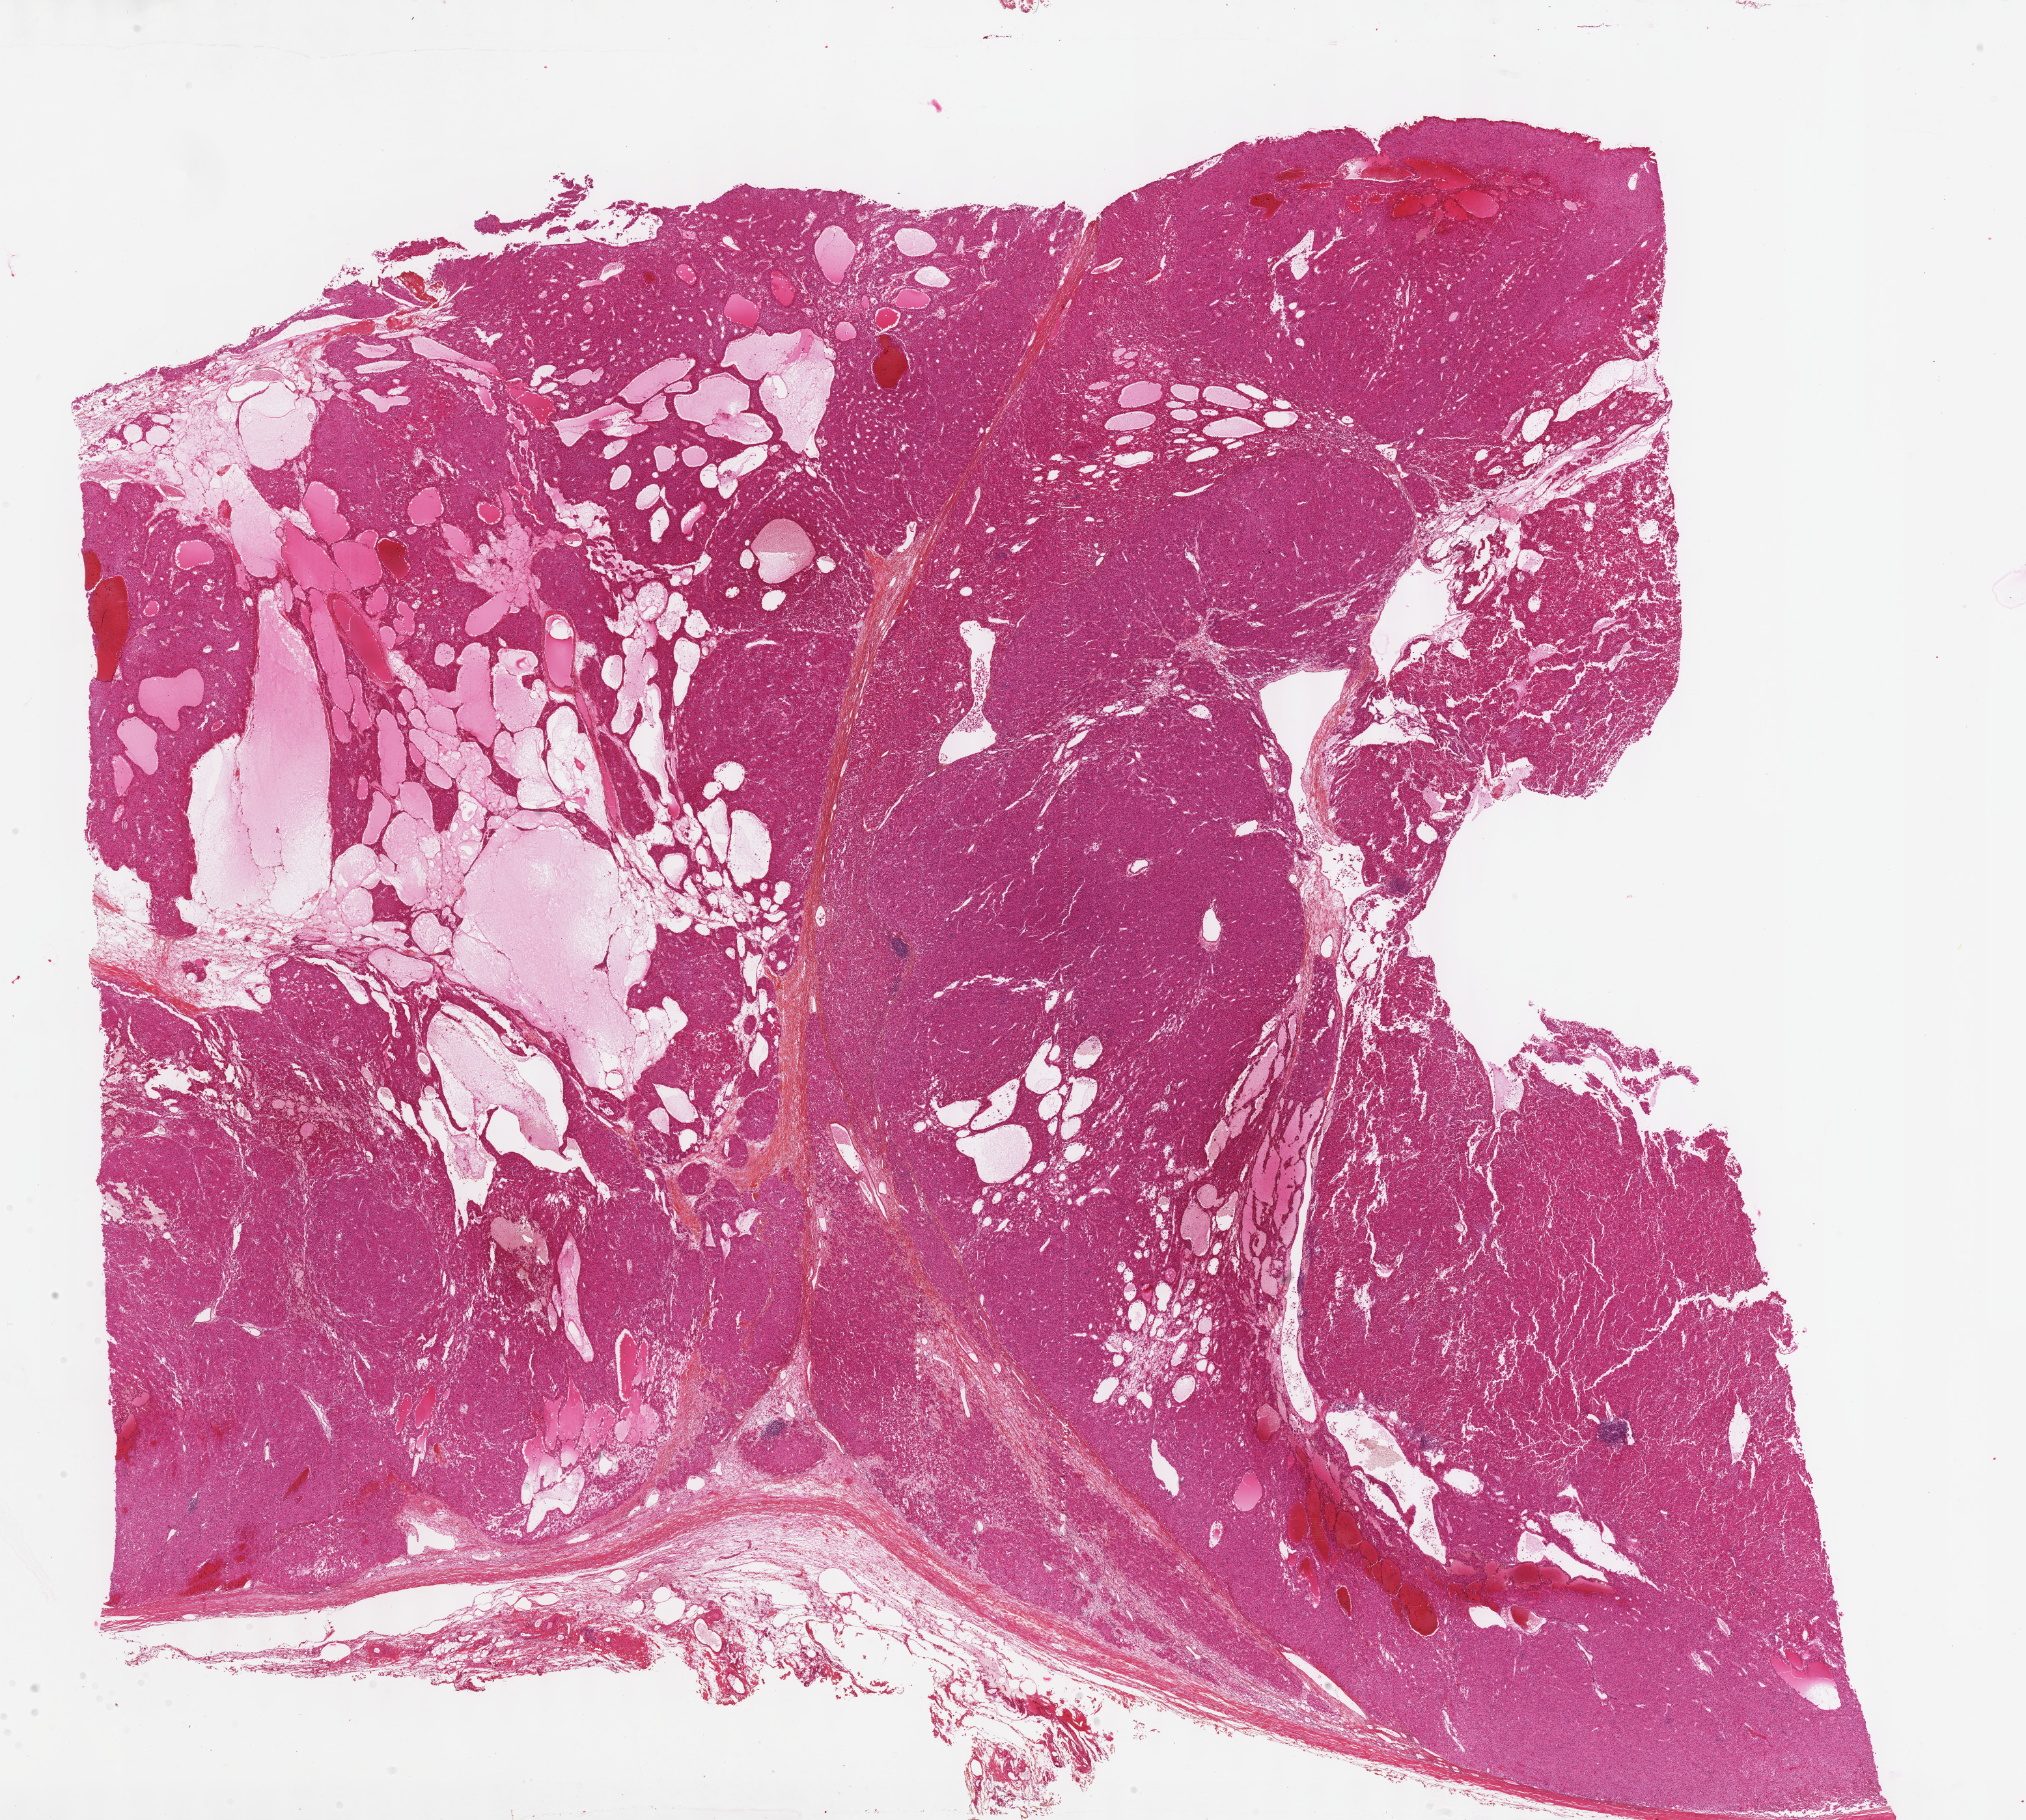
H&E-stained whole-slide image — a low-resolution overview of the entire scanned area, about 25.1 x 22.6 mm (from a 40x scan), formalin-fixed paraffin-embedded (FFPE) diagnostic section, adrenal cortex, primary tumour sample. Patient: male, age at initial diagnosis 62 years.
Pathologic diagnosis: Adrenal cortical carcinoma.